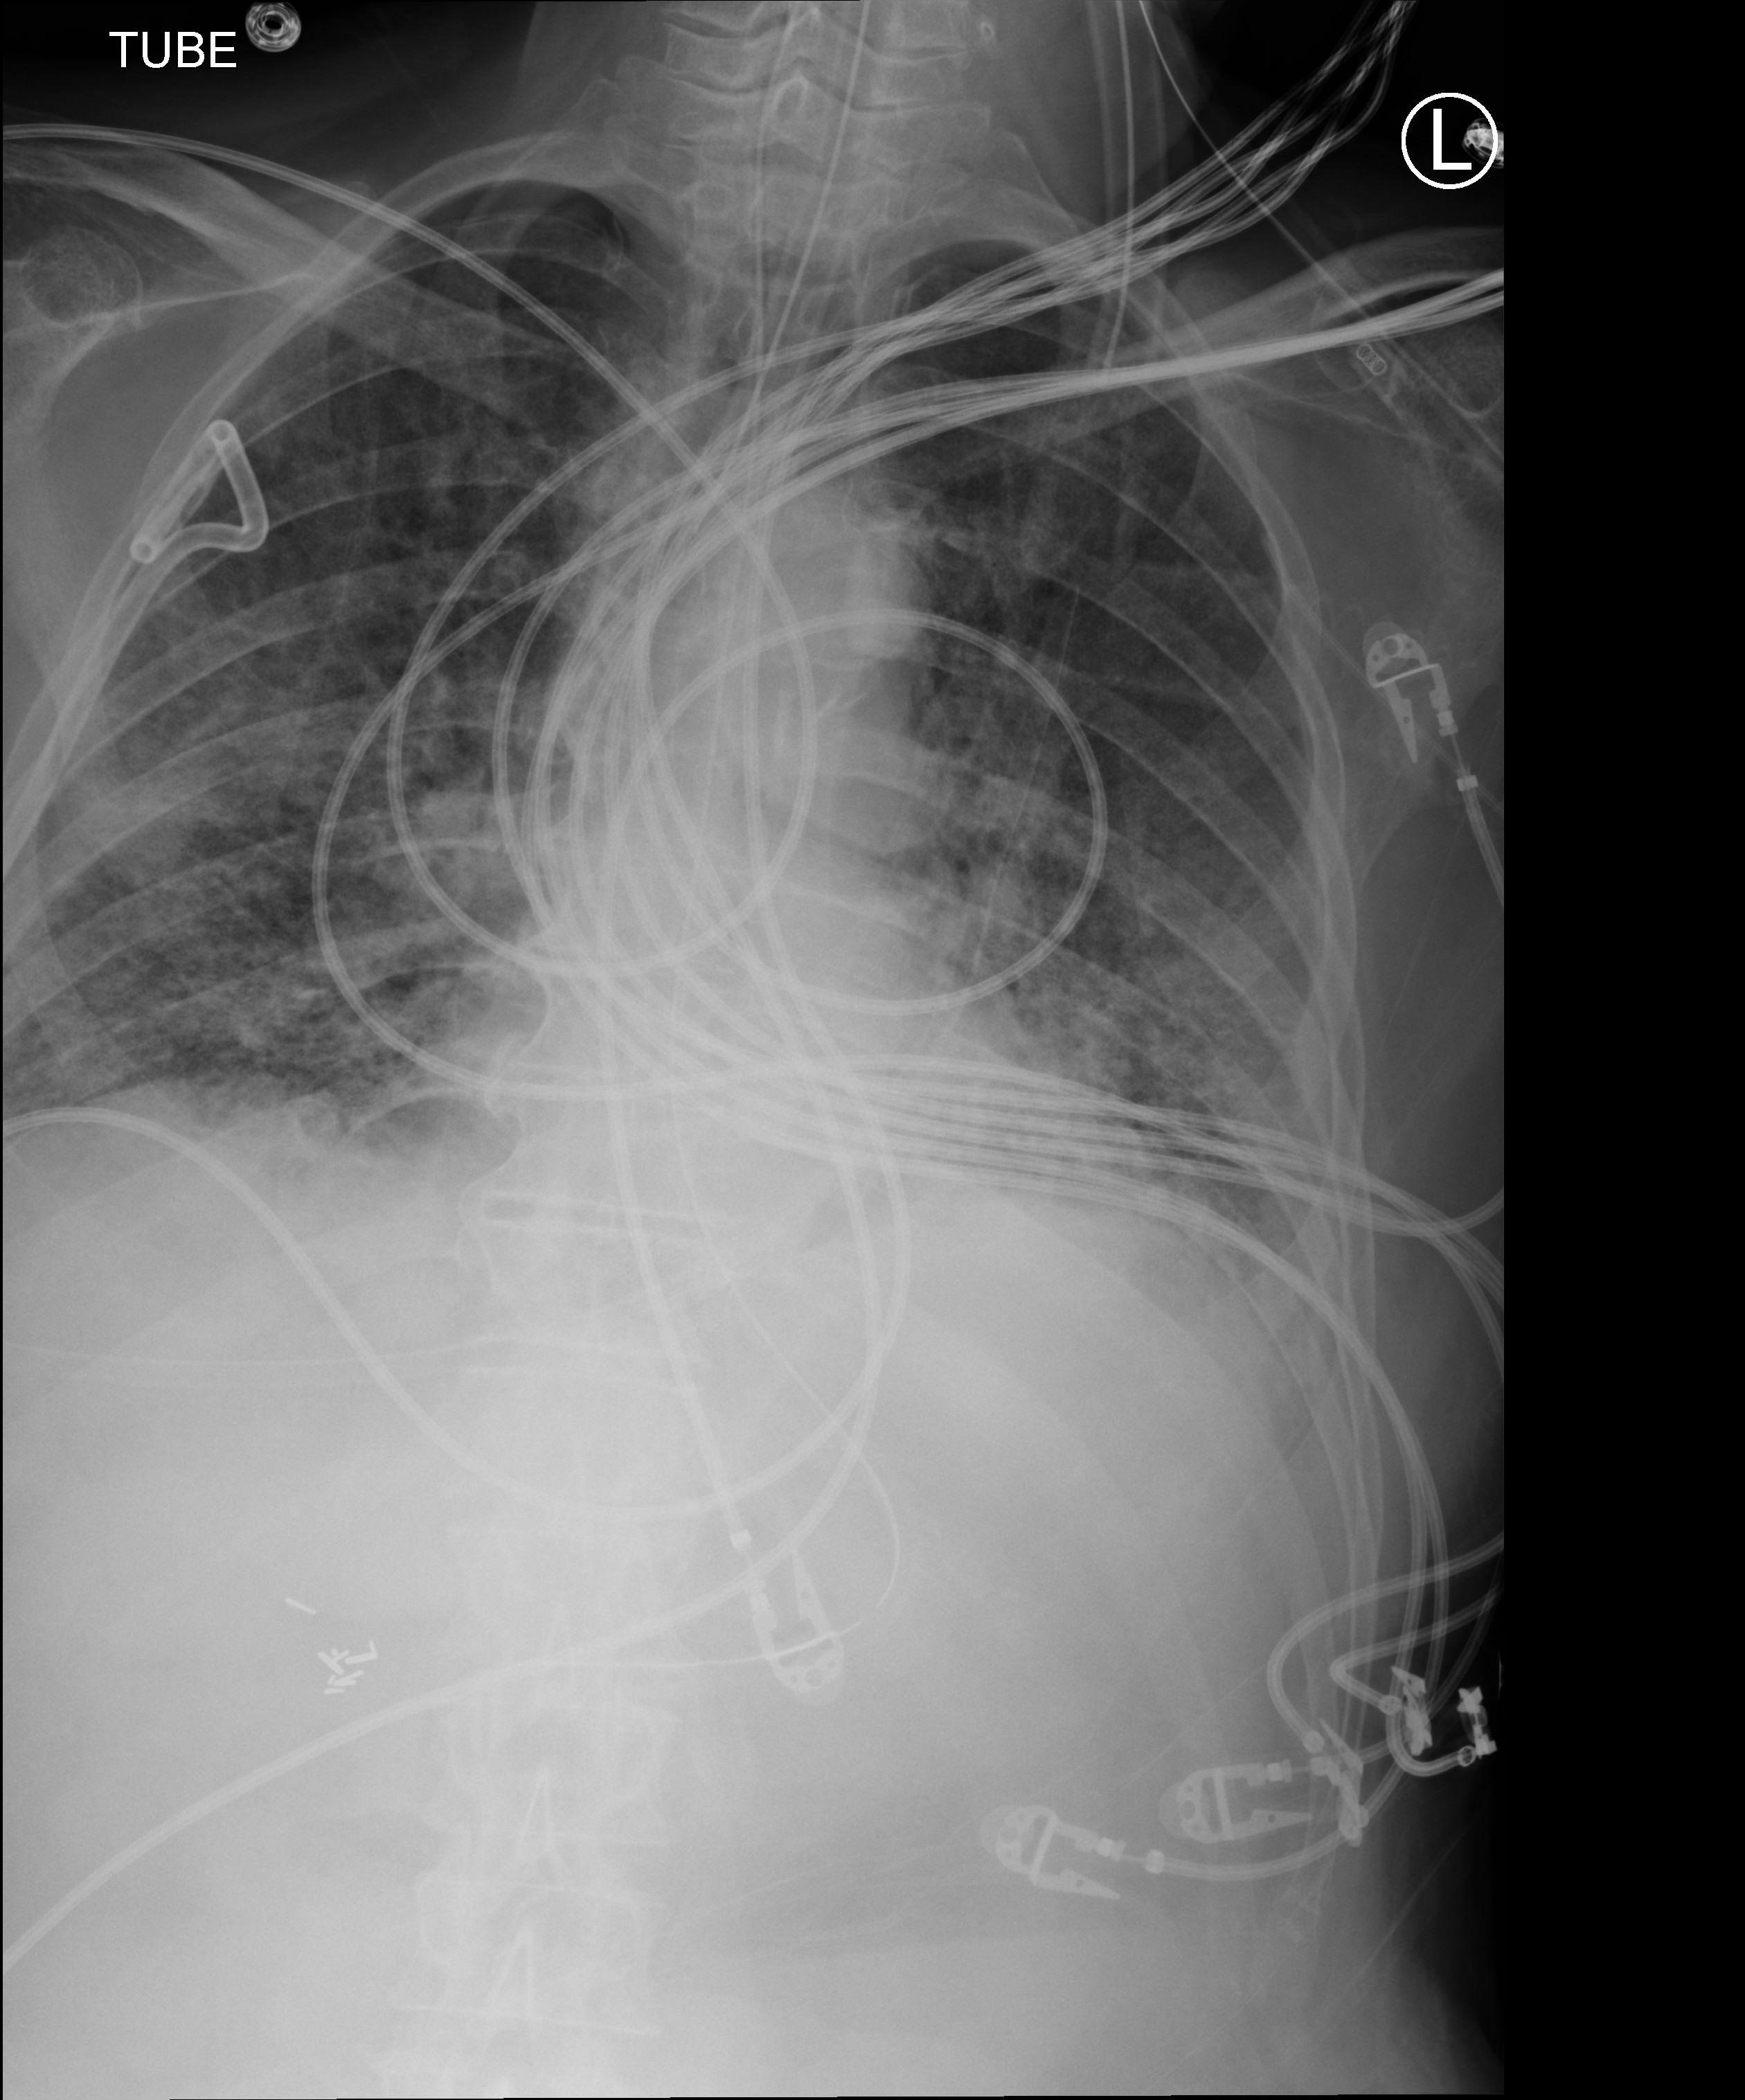
Chest X-ray (portable), anteroposterior (AP) projection. Male patient hospitalised with COVID-19, age 75–90 years.
Hospital-stay facts (about this admission, not read from this image; timing relative to this image not recorded): smoking status (admission record): never; length of hospital stay: 23 days; COPD (admission record): no.